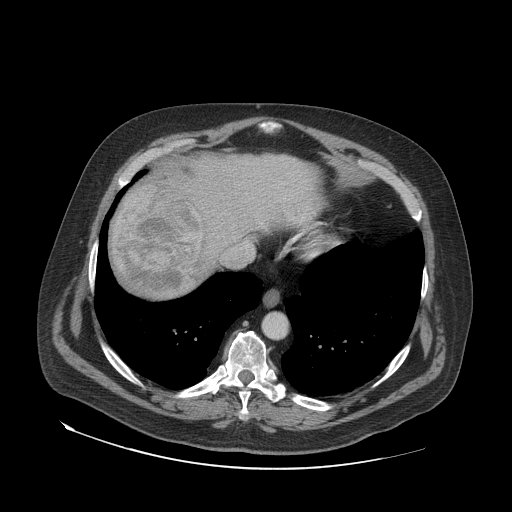
Contrast-enhanced abdominal CT (liver protocol), one axial slice; reconstruction kernel STANDARD; 140 kVp; soft-tissue window (W 400 / L 40 HU); 512 × 512 image matrix, field of view 480 × 480 mm. From the clinical record (not read from this slice): diagnosis: hepatocellular carcinoma (patient treated with transarterial chemoembolisation; whether this scan precedes or follows treatment is not stated here); TNM stage (as recorded): Stage-IVA; Child-Pugh class: A; tumour differentiation: well differentiated.
Structures marked on this image (semi-automatically segmented with operator editing):
- abdominal aorta: bounding box (x1, y1, x2, y2) in pixels: (262, 314, 286, 338)
- liver parenchyma outside the tumour (the mass and vessels are separate outlines, so this box may not span the whole liver): (112, 154, 322, 298)
- mass: (114, 184, 205, 293)